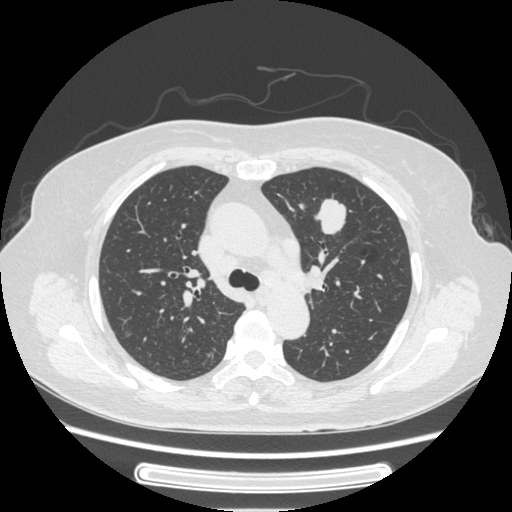
Chest CT, one axial slice. Position 164 of 227 along the scan axis. Reconstruction kernel STANDARD. Lung window (W 1500 / L -600 HU). 1.25 mm slice thickness. 512 × 512 image matrix, field of view 363 × 363 mm. Patient: female, 77 years. From the clinical record (not read from this slice): clinical TNM (as recorded): T1c N3 M0; histopathological grade: G2-3.
Structures marked on this image (rectangle marked by the reading radiologist):
- lung tumour (recorded histology: adenocarcinoma): bounding box <314,196,347,235> (left, top, right, bottom; pixels)